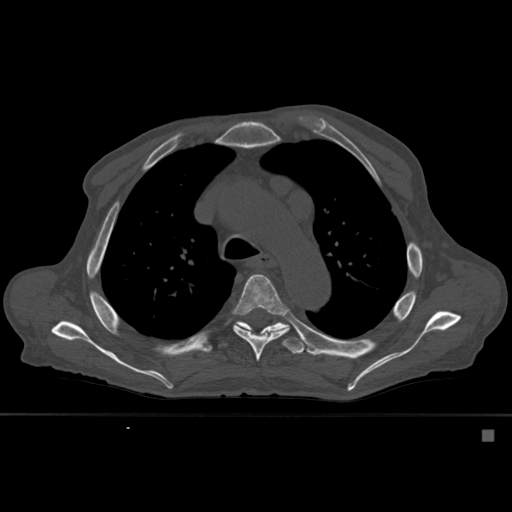
CT including the spine, one axial slice. Slice 398 of 527 in the series (ordered by position). Bone window (W 1800 / L 400 HU). 1.5 mm slice thickness. 512 × 512 image matrix, field of view 373 × 373 mm. Male patient, age 78 years. From the clinical record (not read from this slice): primary cancer: prostate.
Annotated regions visible in this slice (semi-automatically segmented with operator editing):
- T5 vertebra: box from (x=233, y=274) to (x=290, y=362) px
- T6 vertebra: (x=235, y=322)–(x=305, y=354)